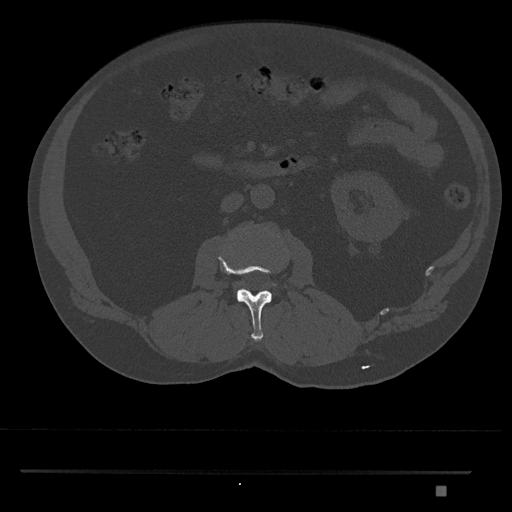
CT including the spine, one axial slice; slice 730 of 1134 in the series (ordered by position); reconstruction kernel Br40s/3; bone window (W 1800 / L 400 HU); 512 × 512 image matrix. Patient: male, 65 years. Case-level facts recorded for this patient, not image findings: primary cancer: prostate.
Outlined on this slice (semi-automatic segmentation, software-assisted and operator-edited):
- L2 vertebra: bounding box <218,255,272,342> (left, top, right, bottom; pixels)
- L3 vertebra: <271,283,276,286>